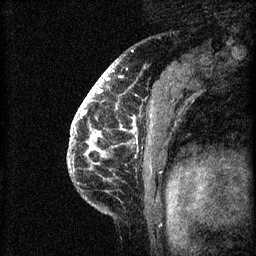
Breast MRI (dynamic contrast-enhanced), one sagittal slice; position 46 of 60 along the scan axis; 3 images stored at this slice position (order not interpretable as contrast timing); 1.5 T; TE 4.2 ms, TR 8.2 ms; 2 mm slice thickness; 256 × 256 image matrix. Female patient, age 41 years.
Structures marked on this image (semi-automatic segmentation, software-assisted and operator-edited):
- analysis volume of interest (the breast-tissue region the enhancement analysis was run in; not a lesion): box from (x=72, y=108) to (x=162, y=205) px
- tumour enhancement mask (voxels above the 70 % enhancement threshold inside the analysis volume of interest): (x=72, y=108)–(x=135, y=151)